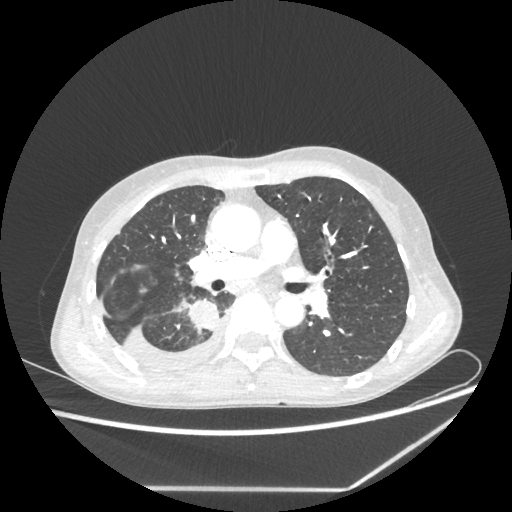
Chest CT, one axial slice; position 134 of 237 along the scan axis; 80 kVp; lung window (W 1500 / L -600 HU); 512 × 512 image matrix, field of view 364 × 364 mm. Patient: female, 59 years. Case-level facts recorded for this patient, not image findings: clinical TNM (as recorded): T1c N1 M1.
Structures marked on this image (rectangle marked by the reading radiologist):
- lung tumour (recorded histology: adenocarcinoma): bounding box [x1, y1, x2, y2] px = [186, 296, 220, 336]